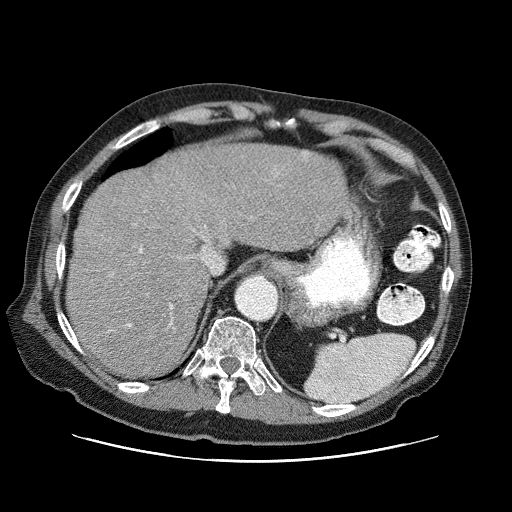
Contrast-enhanced abdominal CT (liver protocol), one axial slice; slice 58 of 87 in the series (ordered by position); 120 kVp; one of 3 acquisitions stored at this slice position; soft-tissue window (W 400 / L 40 HU); 512 × 512 image matrix, field of view 400 × 400 mm. Case-level facts recorded for this patient, not image findings: diagnosis: hepatocellular carcinoma (patient treated with transarterial chemoembolisation; whether this scan precedes or follows treatment is not stated here); TNM stage (as recorded): Stage-IIIA; Child-Pugh class: A; tumour nodularity: multinodular; tumour size: 6 cm.
Annotated regions visible in this slice (semi-automatically segmented with operator editing):
- abdominal aorta: bounding box <238,276,276,319> (left, top, right, bottom; pixels)
- liver parenchyma outside the tumour (the mass and vessels are separate outlines, so this box may not span the whole liver): <66,144,352,376>
- liver vessels: <127,225,206,327>